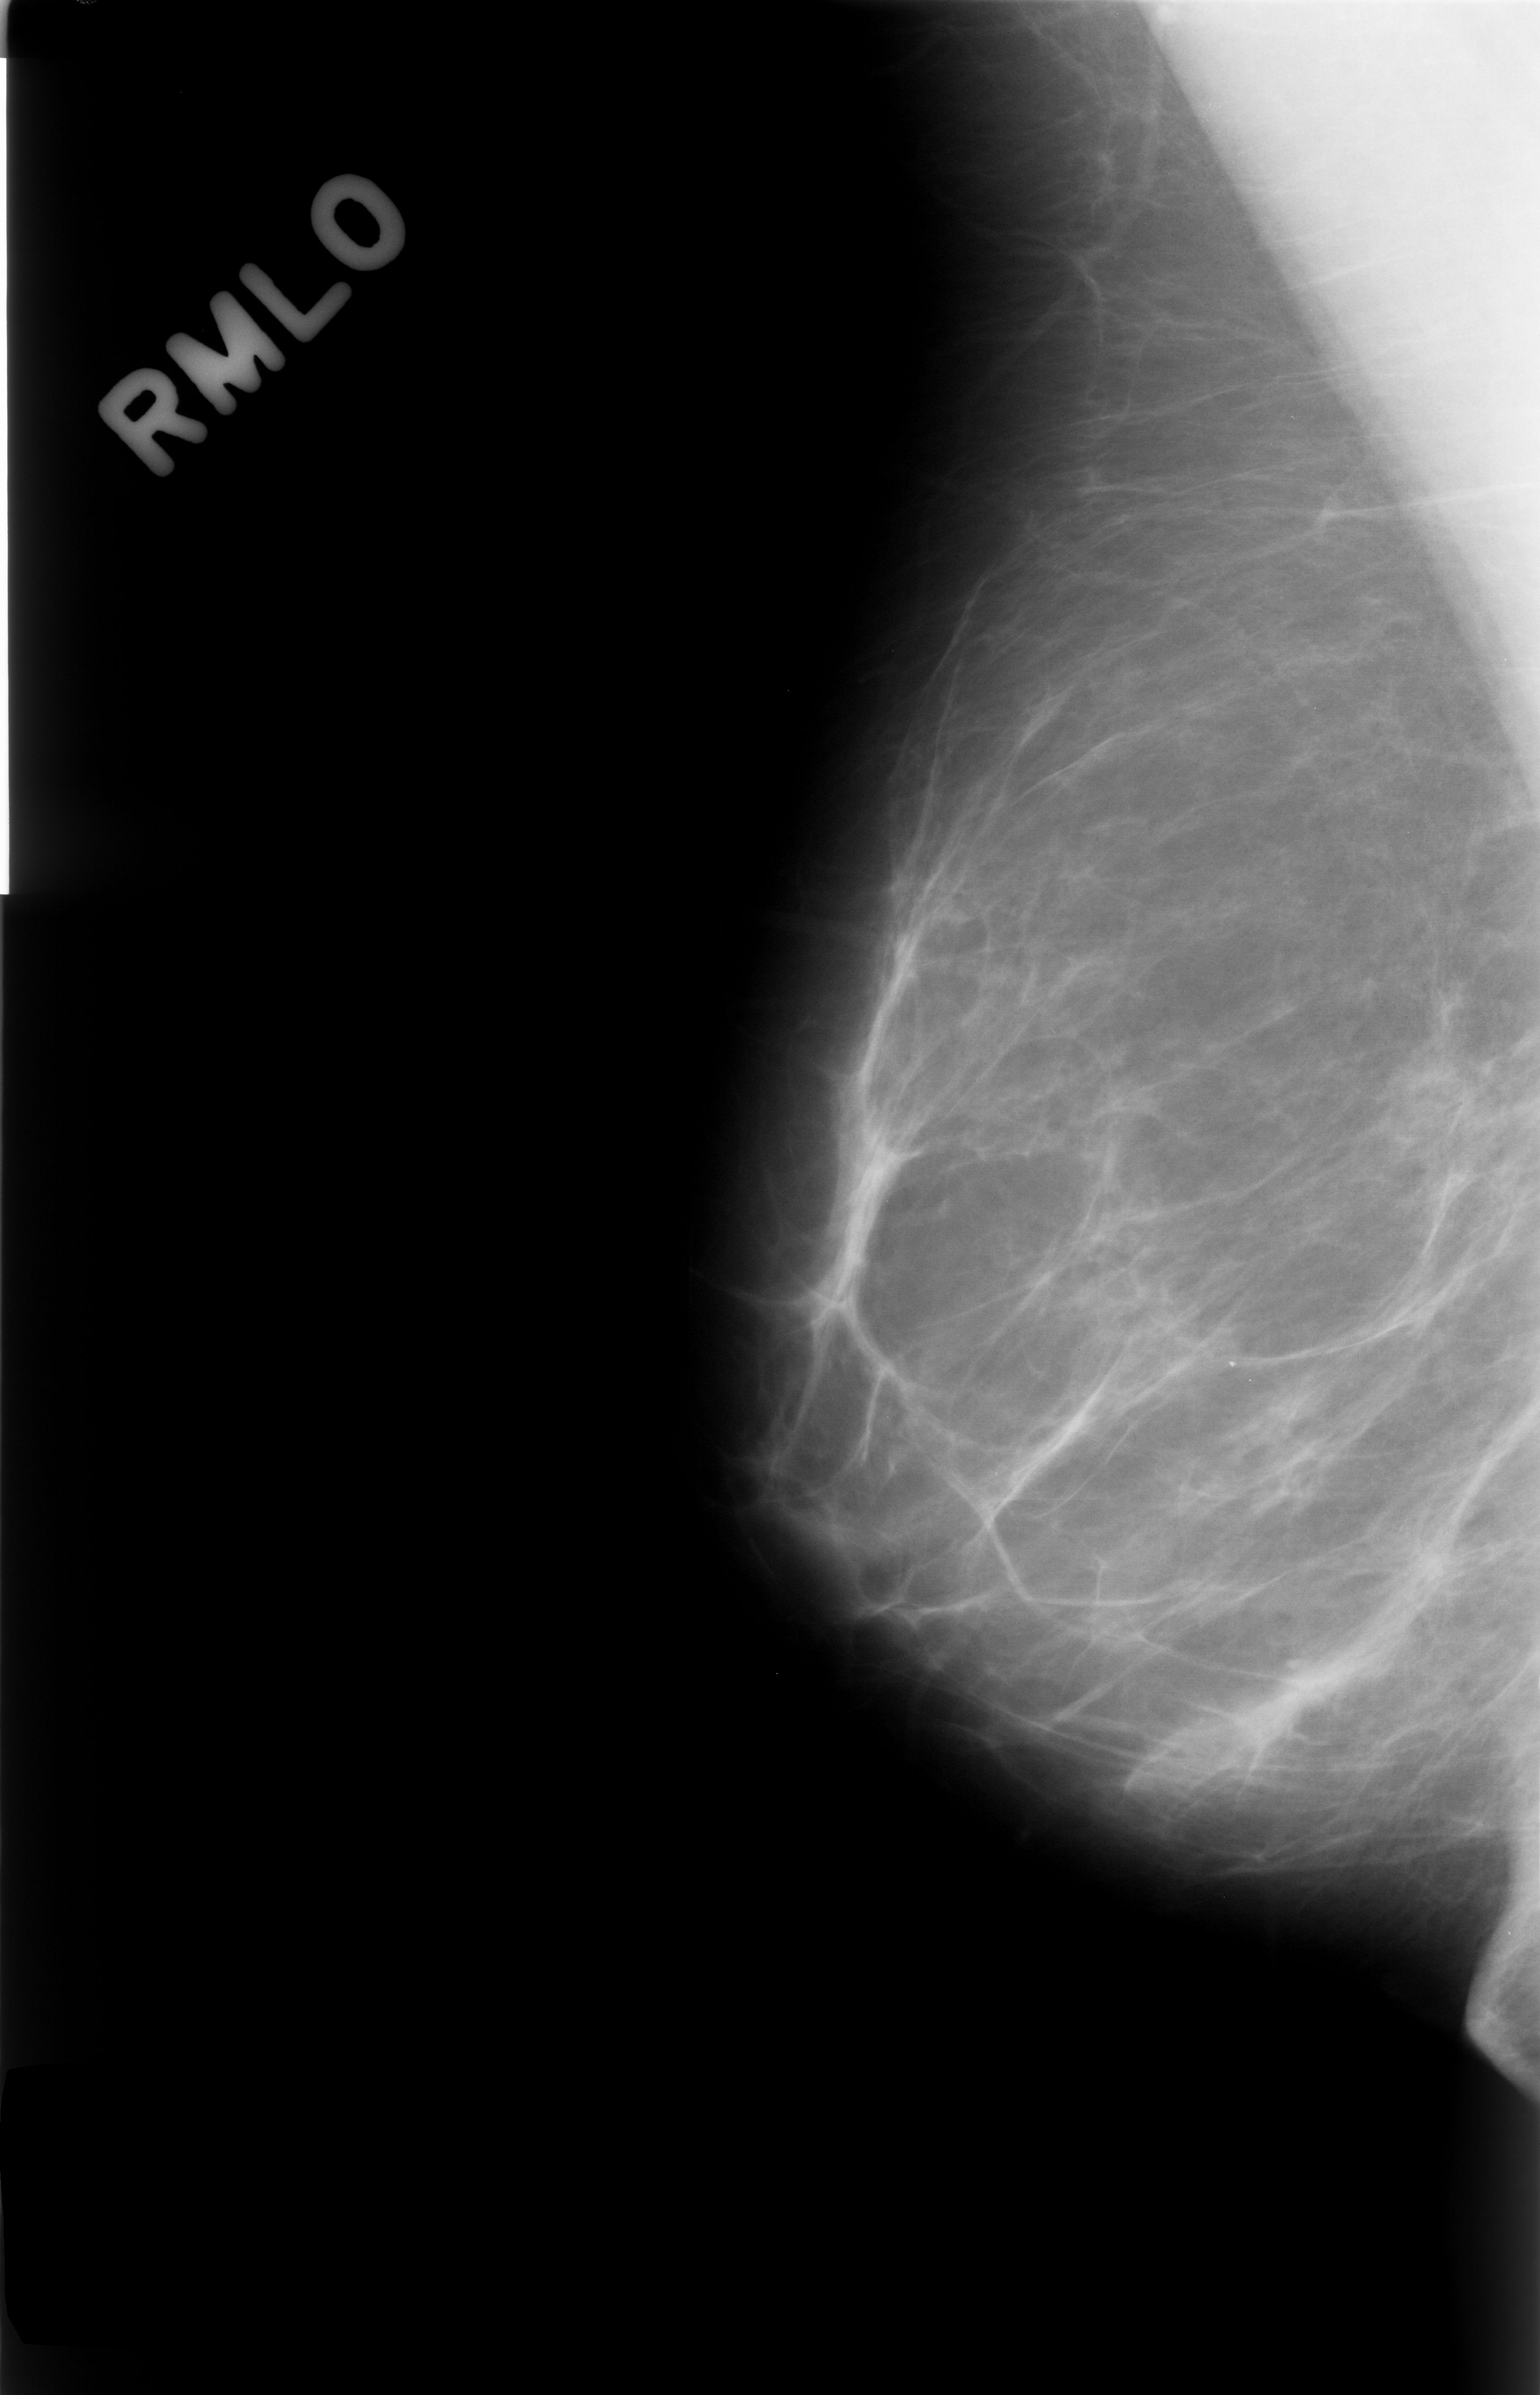
Scanned film-screen mammogram; right breast; MLO view; breast composition: almost entirely fatty (BI-RADS density category 1 of 4).
Abnormality record for this image: mass, shape focal asymmetric density; BI-RADS assessment category 3; benign without callback (not worked up further).